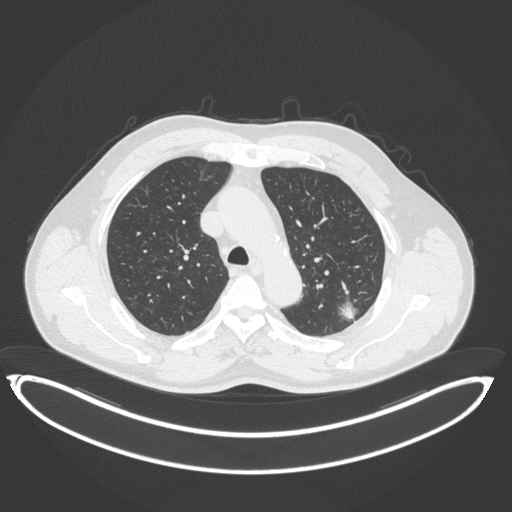
Chest CT, one axial slice. Position 263 of 399 along the scan axis. Reconstruction kernel B31f. Lung window (W 1500 / L -600 HU). 1 mm slice thickness. 512 × 512 image matrix, field of view 469 × 469 mm. Male patient, age 58 years. From the clinical record (not read from this slice): clinical TNM (as recorded): T1c N0 M0; histopathological grade: G1-2.
Outlined on this slice (bounding box drawn by a radiologist):
- lung tumour (recorded histology: adenocarcinoma): bounding box (x1, y1, x2, y2) in pixels: (335, 297, 362, 328)